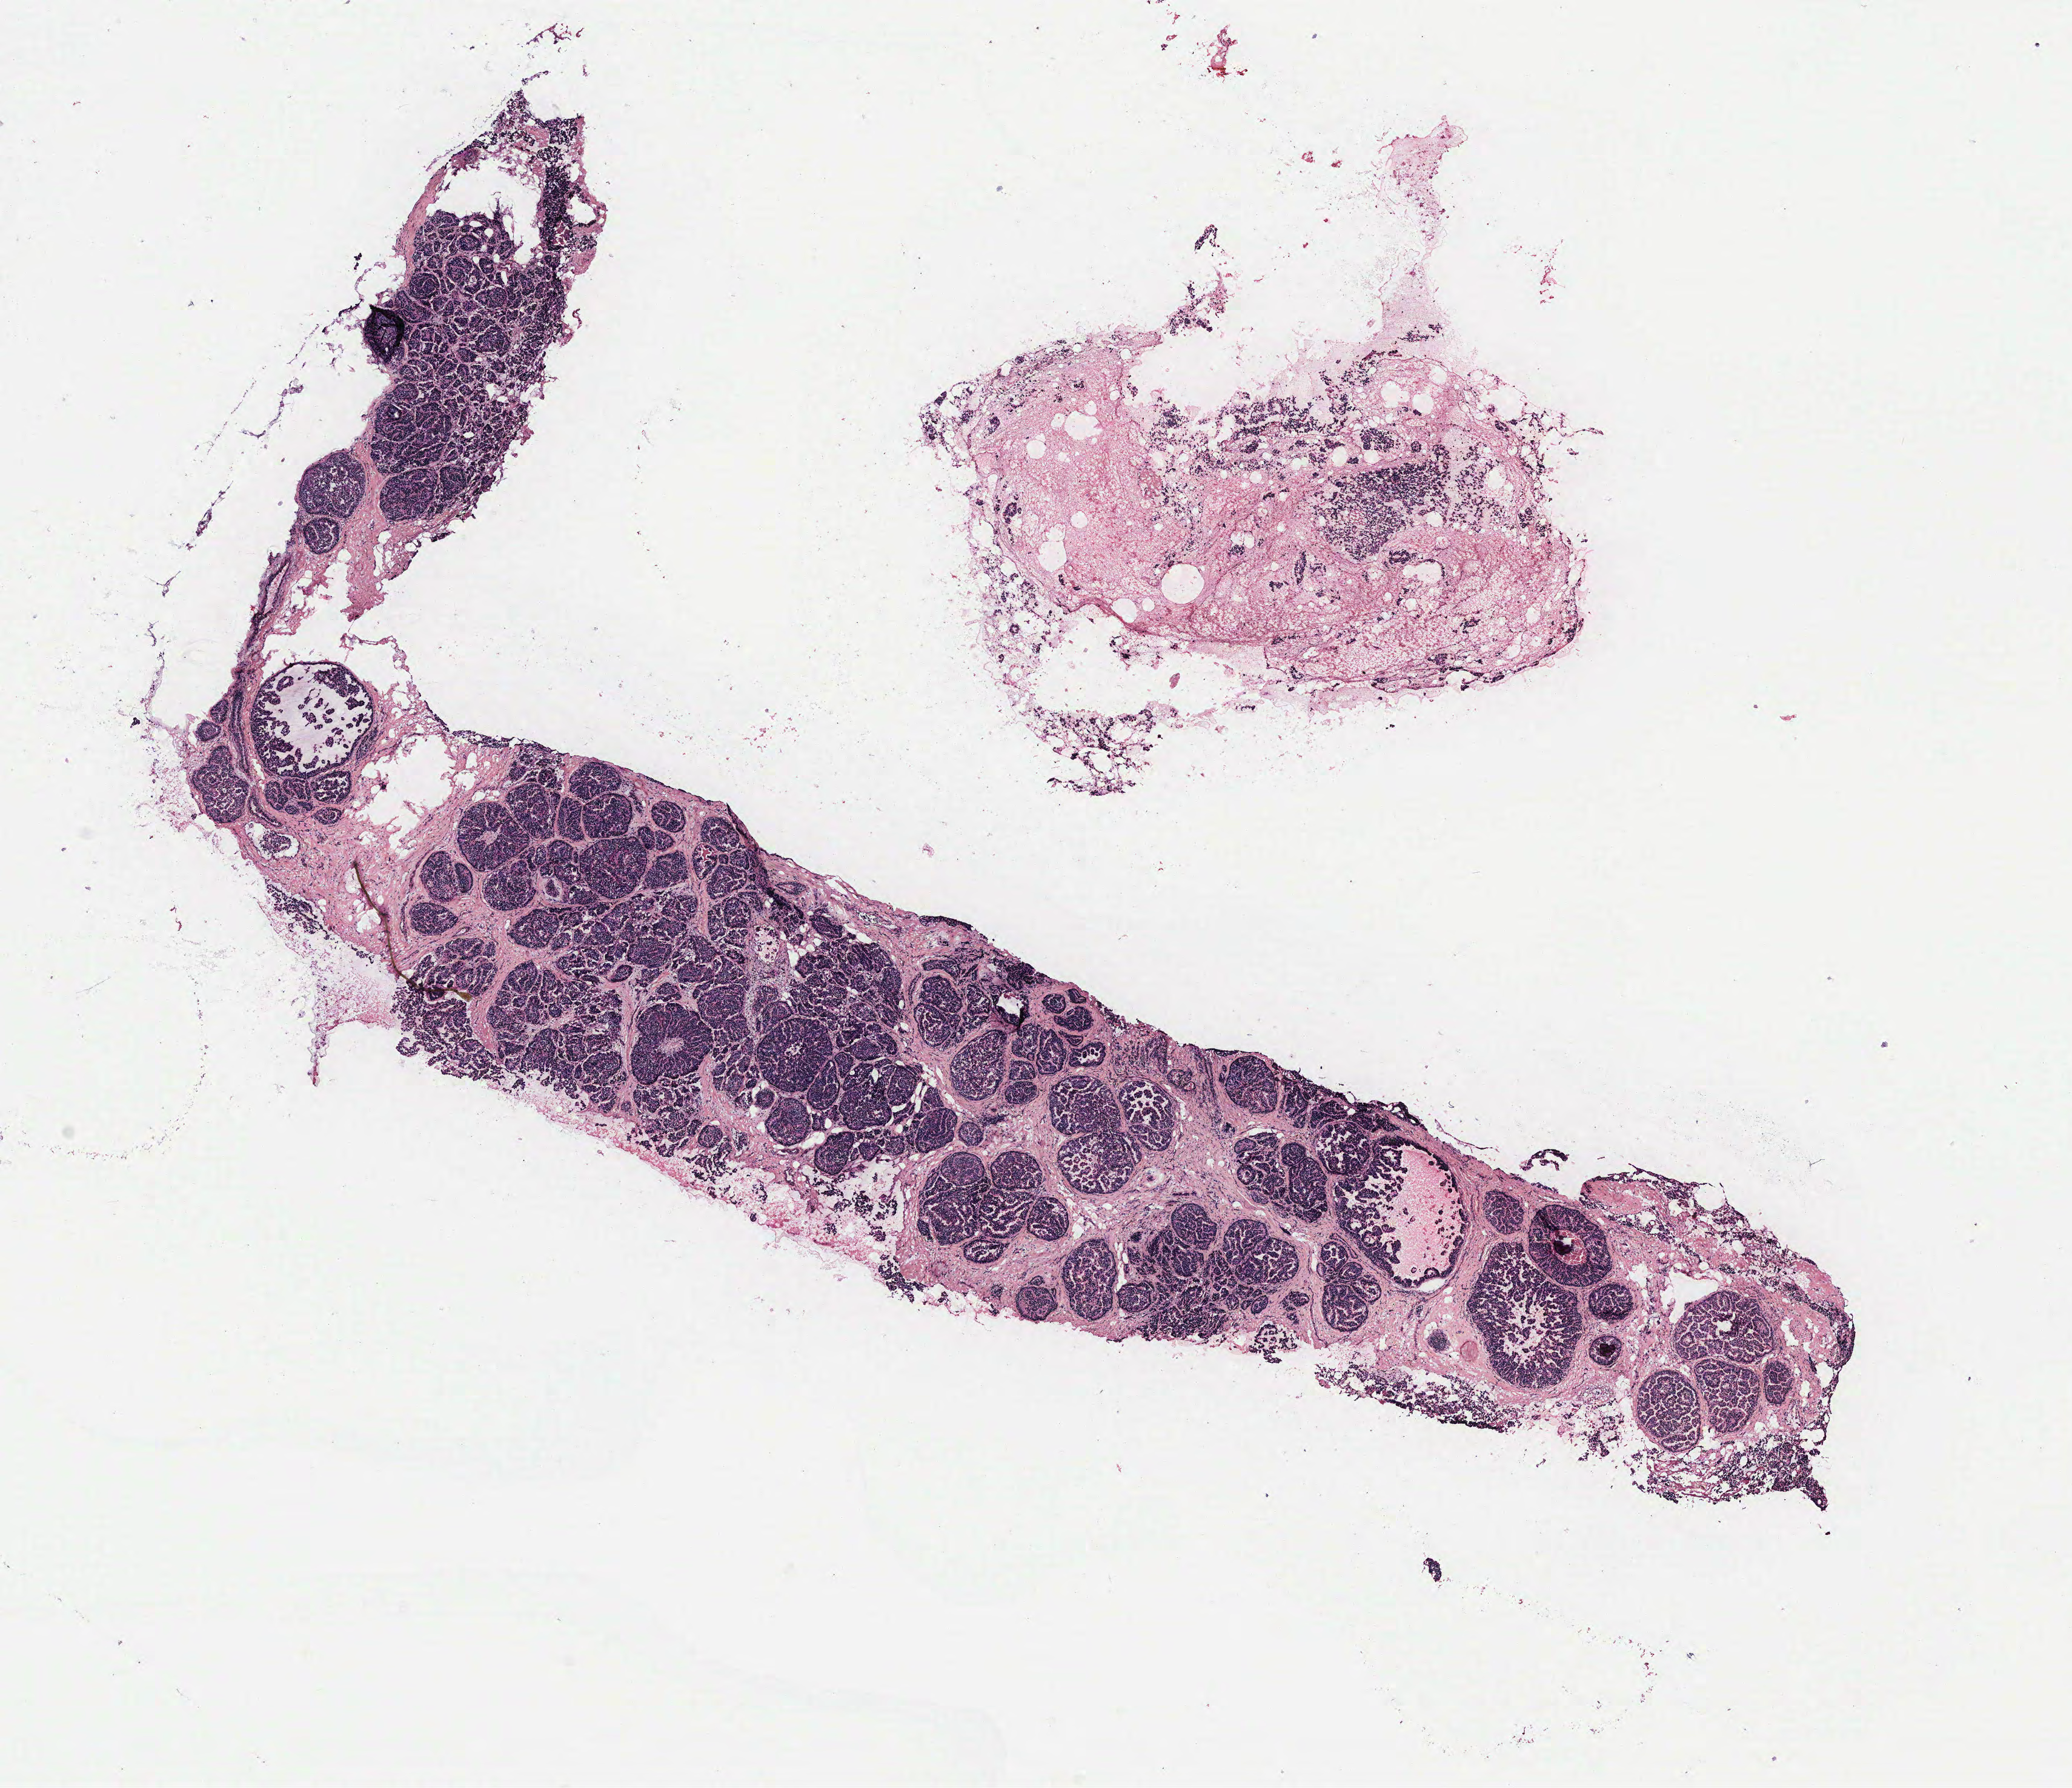
Digitized H&E-stained tissue section (whole slide), shown as a low-resolution overview of the whole scanned area (about 13.7 x 11.8 mm, from a 40x scan). 52-year-old female patient.
- specimen: breast, tumour tissue